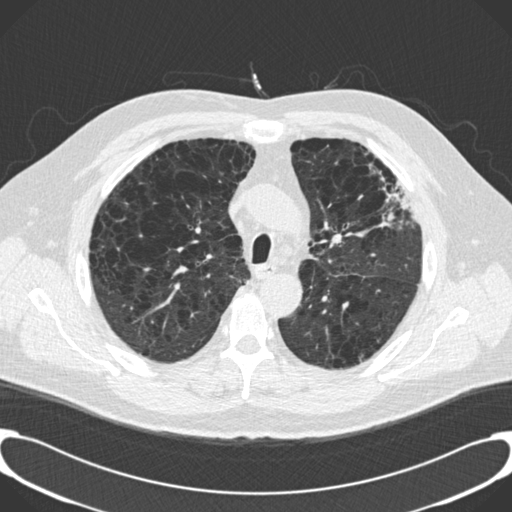
Chest CT (low-dose screening protocol), one axial image; third annual screen; lung window (W 1500 / L -600 HU); 2 mm slice thickness. Male participant, aged 59 years at enrolment.
Expert reader's lesion annotation, bounding box [x1, y1, x2, y2] px = [359, 154, 418, 223]. Screening reader's record for this exam: no non-calcified nodule ≥4 mm recorded. Official screen result: positive, other. Participant outcome: lung cancer diagnosed 134 days after this screen — bronchiolo-alveolar carcinoma, mixed mucinous and non-mucinous, left upper lobe, stage IA (AJCC 6th edition), 20 mm at pathology.